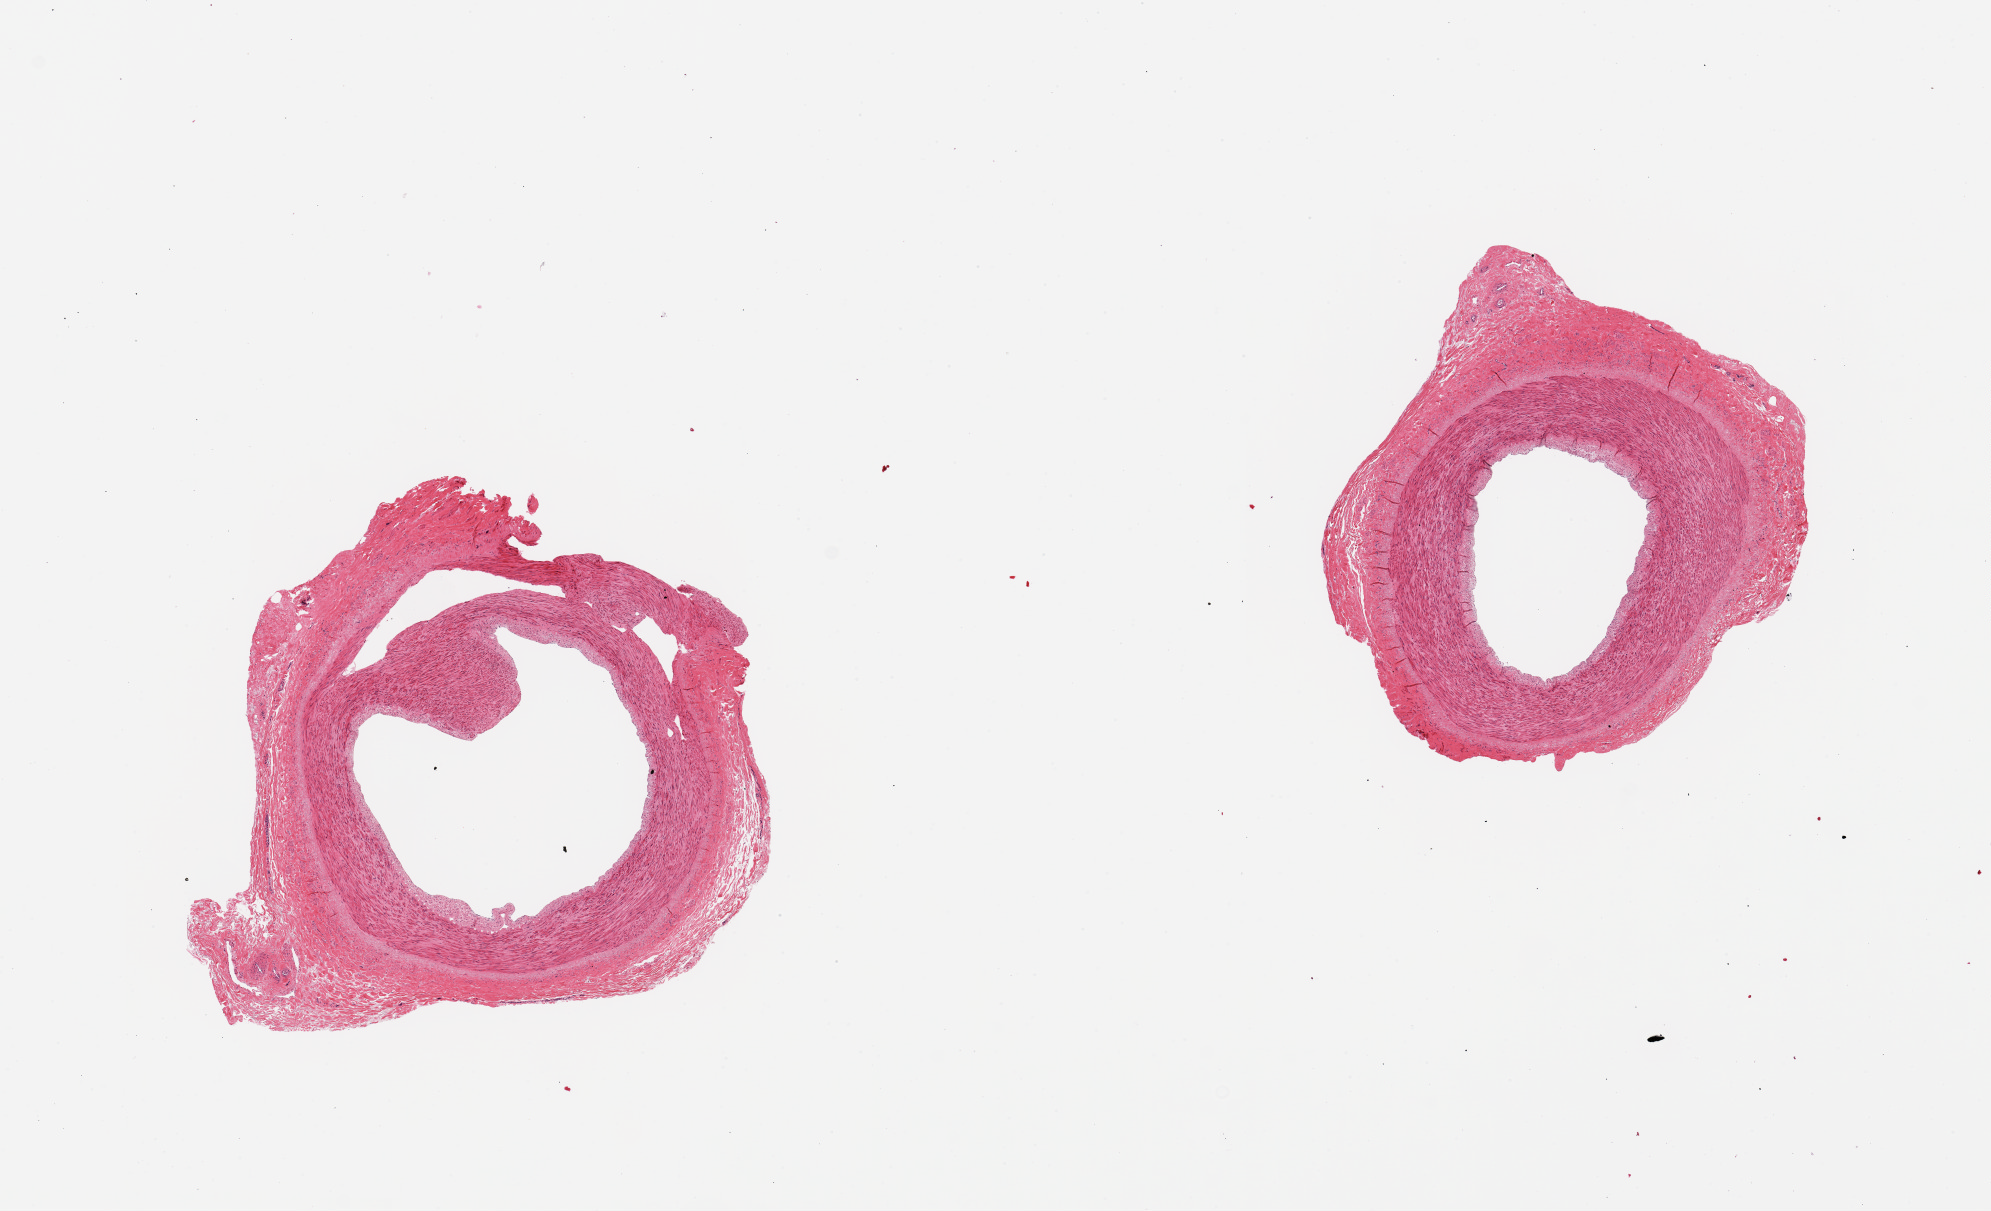
H&E whole-slide image — whole scanned area (about 15.8 x 9.6 mm, slide scanned at 20x) shown as a low-resolution overview; PAXgene-fixed, paraffin-embedded tissue; section of tibial artery (target tissue); tissue donor sample. Female donor.
* reviewer comment on this tissue sample: 2 pieces, clean specimens